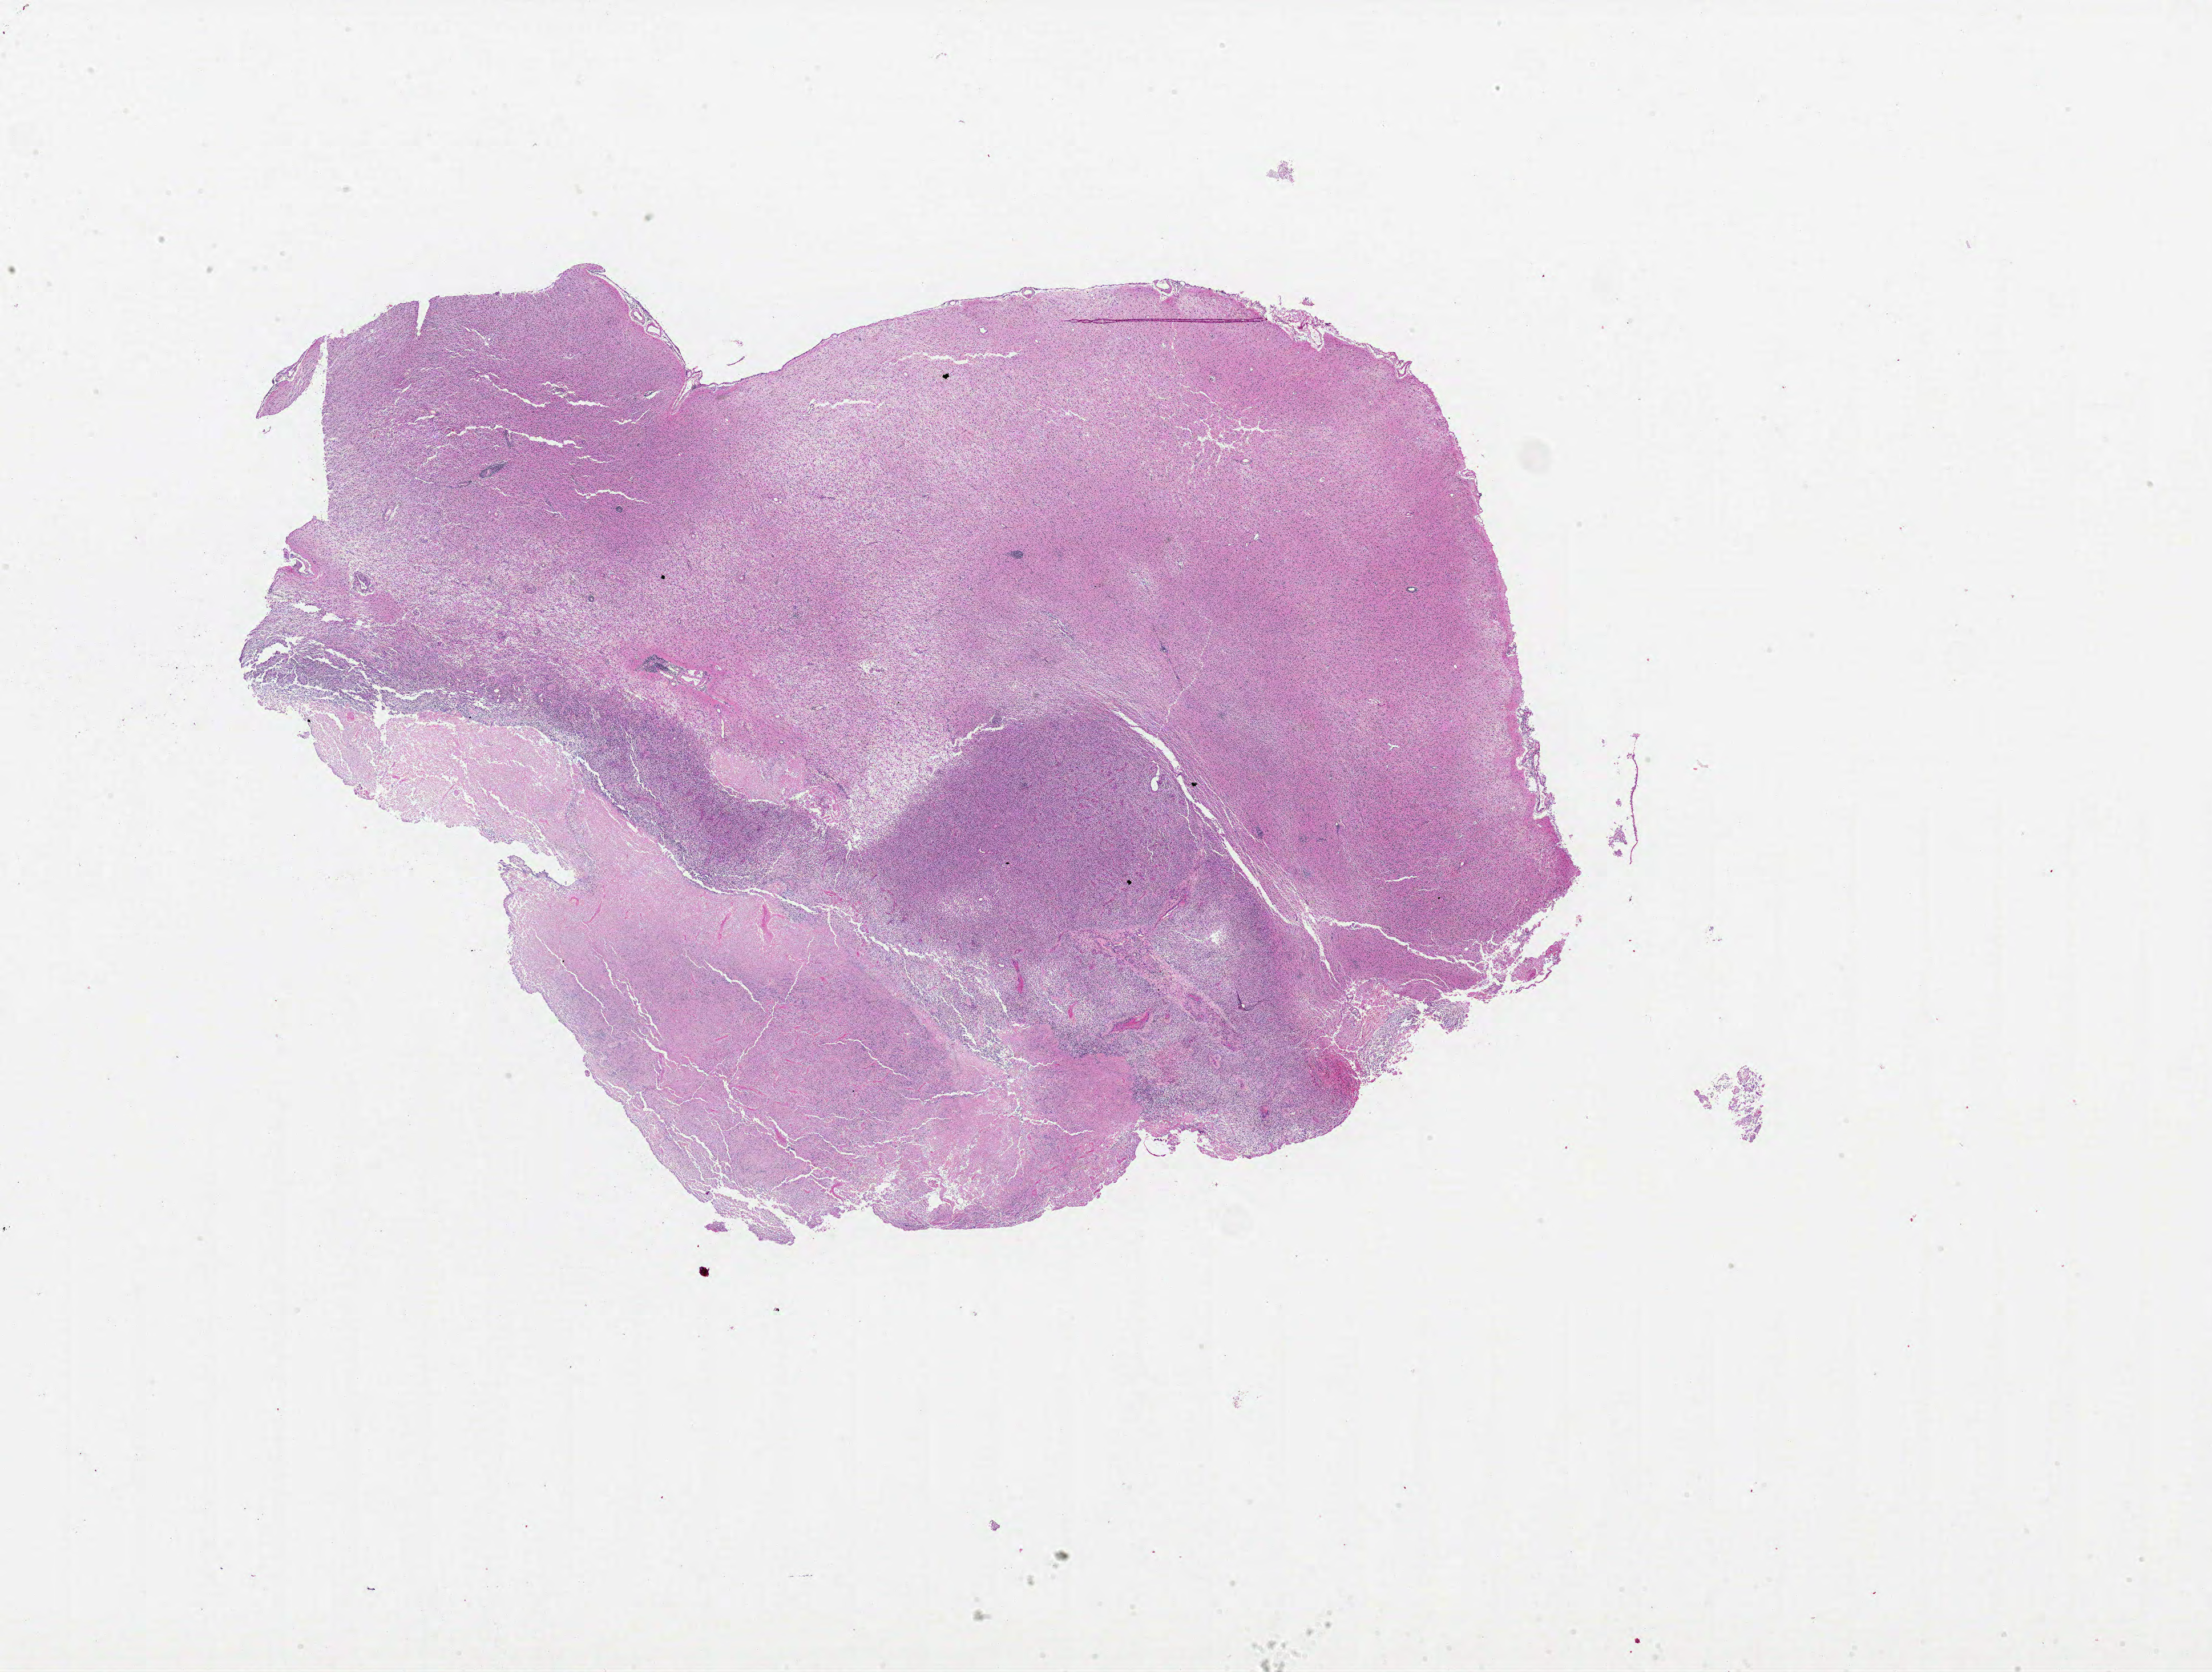
H&E whole-slide image — low-resolution overview of the scanned area, about 31.0 x 23.4 mm (slide scanned at 20x); formalin-fixed paraffin-embedded (FFPE) diagnostic section; sample: primary tumour, brain. Patient: male, age at initial diagnosis 75 years.
Histologic diagnosis: Glioblastoma.